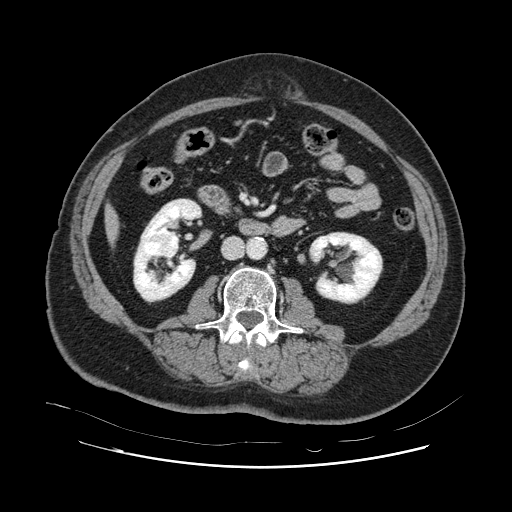
Contrast-enhanced abdominal CT, one axial slice. Slice 19 of 132 in the series (ordered by position). 120 kVp. Intravenous contrast given. Soft-tissue window (W 400 / L 40 HU). 2.5 mm slice thickness. 512 × 512 image matrix, field of view 391 × 391 mm. Female patient, age 73 years. From the clinical record (not read from this slice): diagnosis: colorectal cancer liver metastases, imaged before liver resection; multiple liver metastases: no; largest metastasis: 7 cm.
Structures marked on this image (manually delineated by an expert):
- liver: bounding box [x1, y1, x2, y2] px = [108, 212, 117, 236]
- planned liver remnant (the part of the liver to remain after resection): [108, 210, 118, 237]